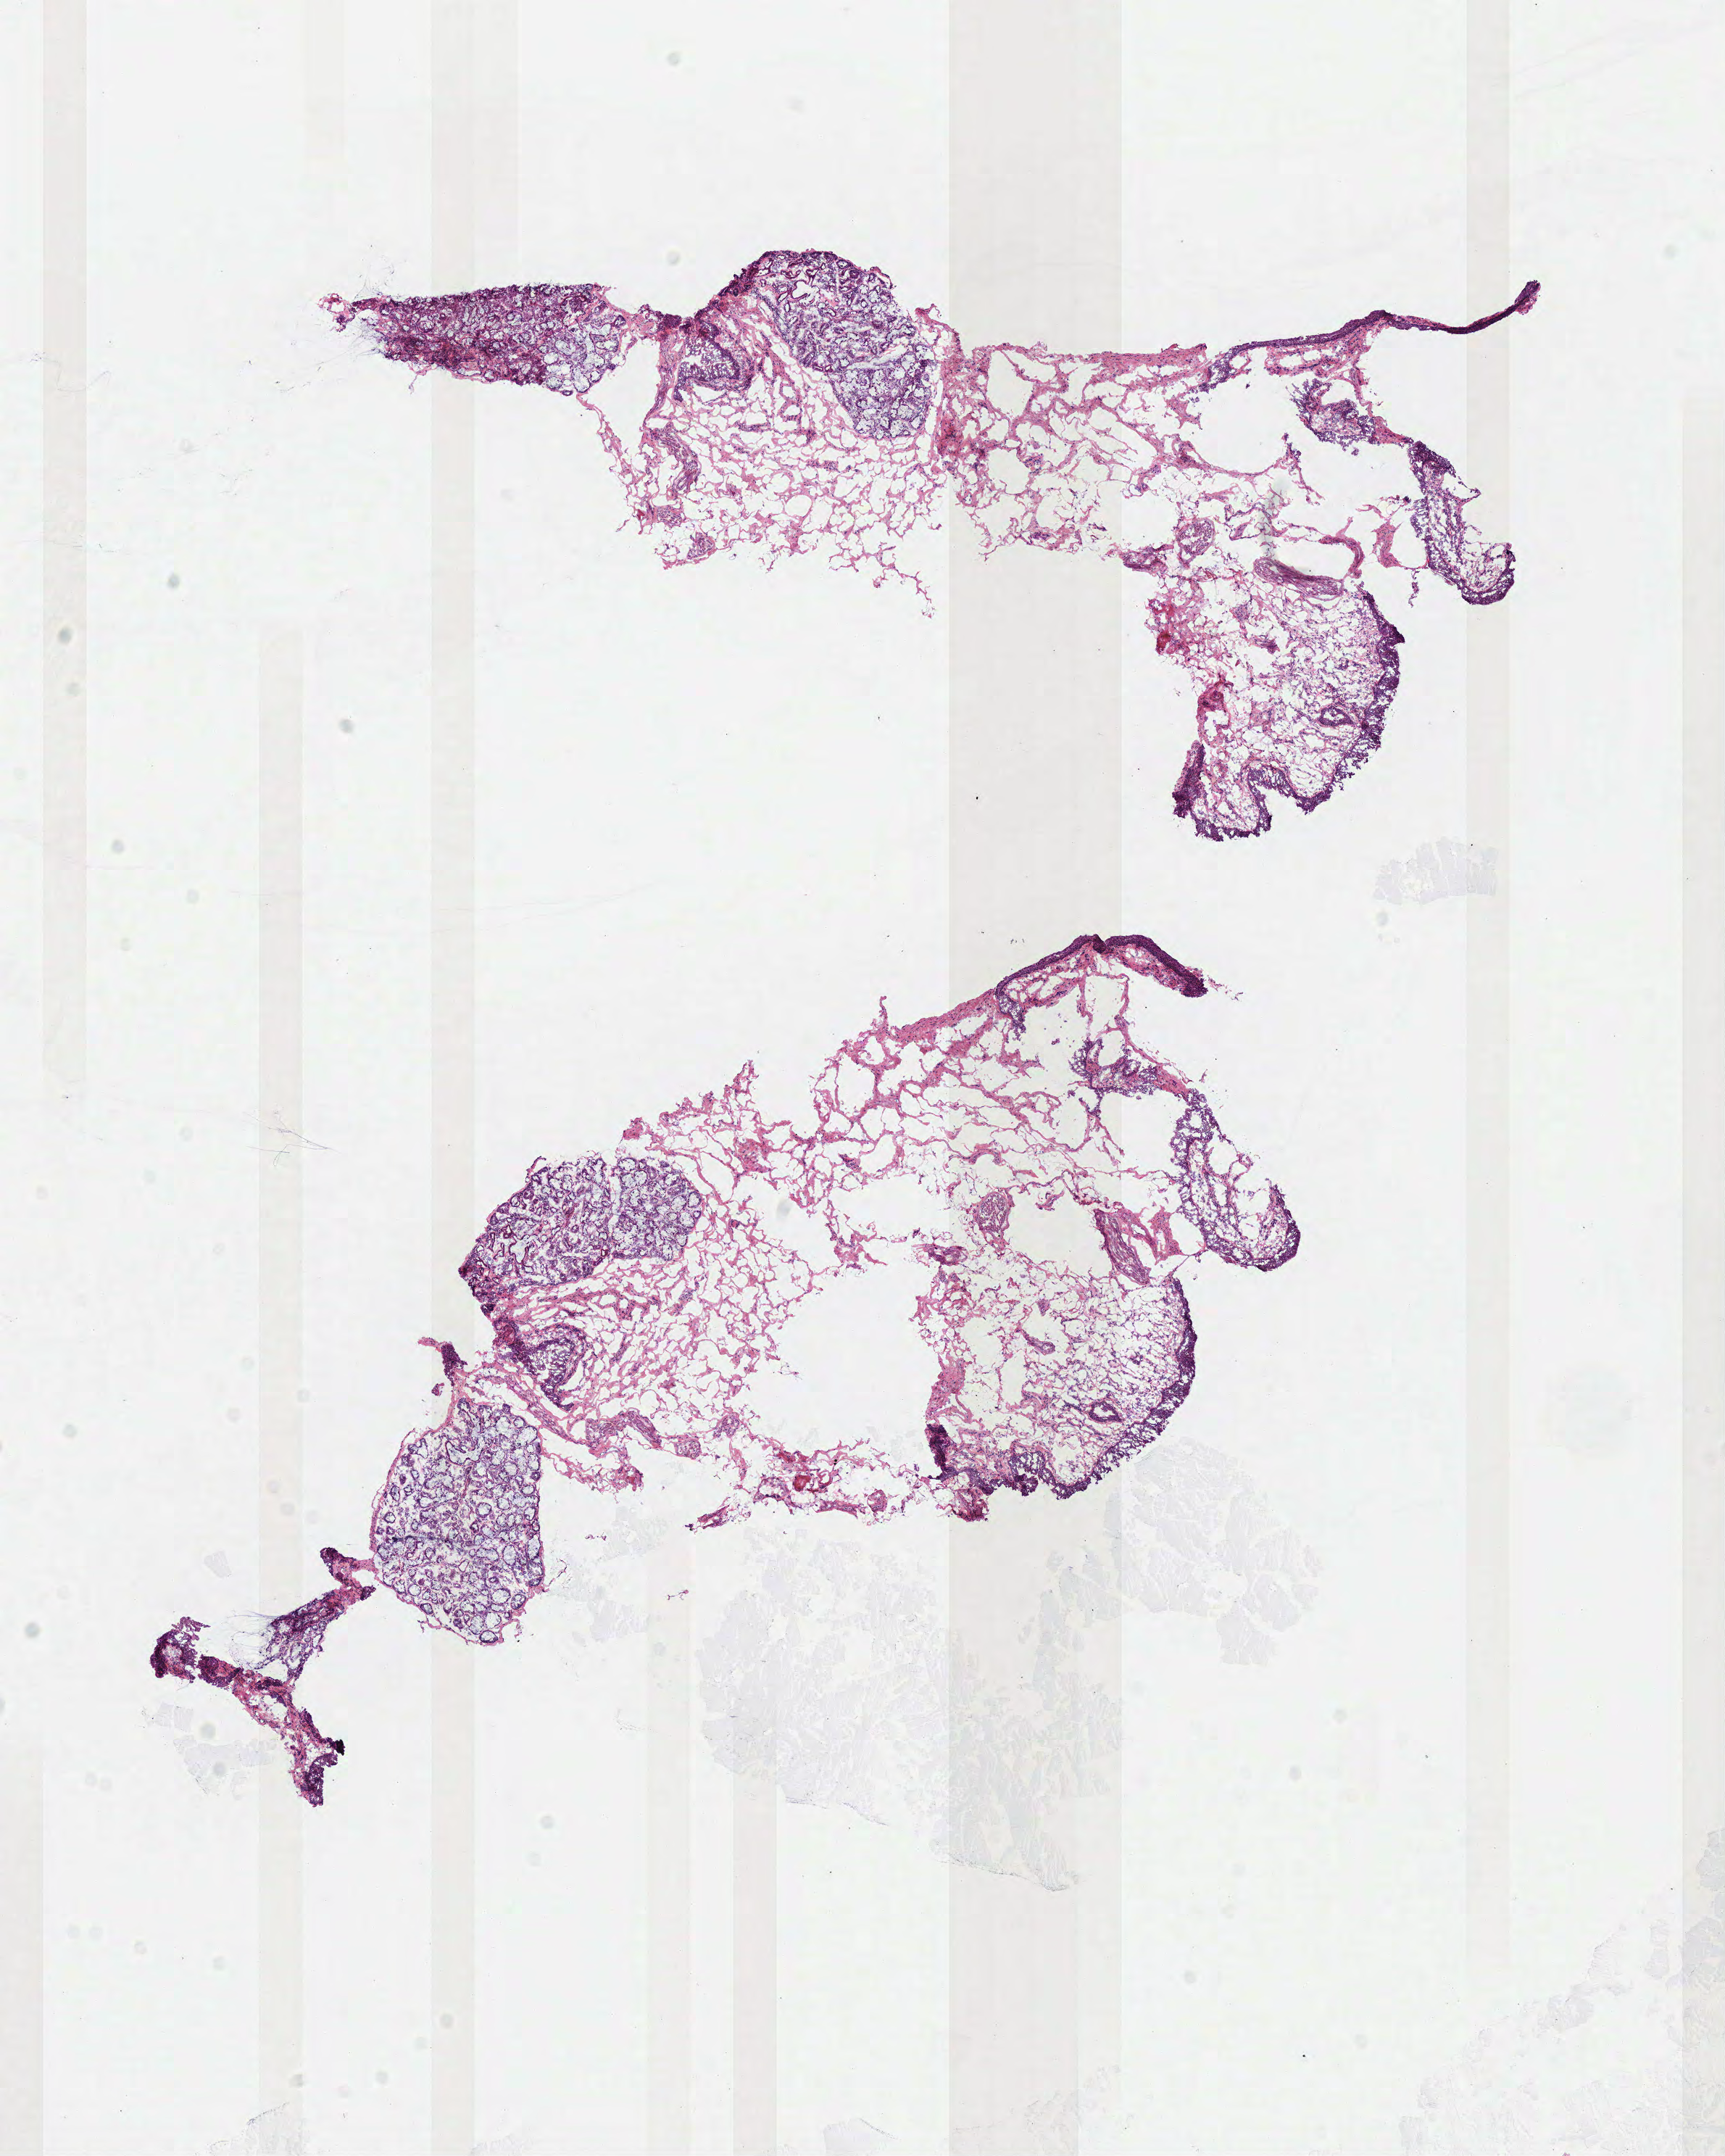
Whole-slide histology image, H&E — low-resolution overview of the scanned area, about 9.4 x 11.7 mm (acquisition: 40x scan); frozen section from the top of the tissue portion; head and neck, solid tissue normal (non-tumour tissue) sample. Female patient; age at initial diagnosis 66 years.
- this section: solid tissue normal sample (biorepository sample class)
- patient diagnosis: Squamous cell carcinoma, NOS